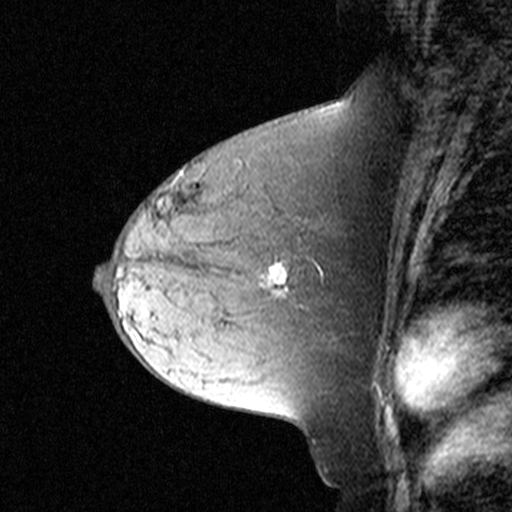
Breast MRI (dynamic contrast-enhanced), one sagittal slice. Slice 17 of 44 in the series (ordered by position). Dynamic contrast-enhanced study with each time point stored as its own series, time point 2 of 3 at this slice position (early post-contrast, ordered by acquisition time). 1.5 T. TE 4.5 ms, TR 11 ms. 3 mm slice thickness. 512 × 512 image matrix. Patient: female, 44 years. Case-level facts recorded for this patient, not image findings: setting: breast cancer imaged before/during neoadjuvant chemotherapy; receptor status: triple-negative.
Annotated regions visible in this slice (semi-automatic segmentation, software-assisted and operator-edited):
- analysis volume of interest (the breast-tissue region the enhancement analysis was run in; not a lesion): box from (x=174, y=204) to (x=303, y=305) px
- tumour enhancement mask (voxels above the 90 % enhancement threshold inside the analysis volume of interest): (x=267, y=265)–(x=287, y=294)